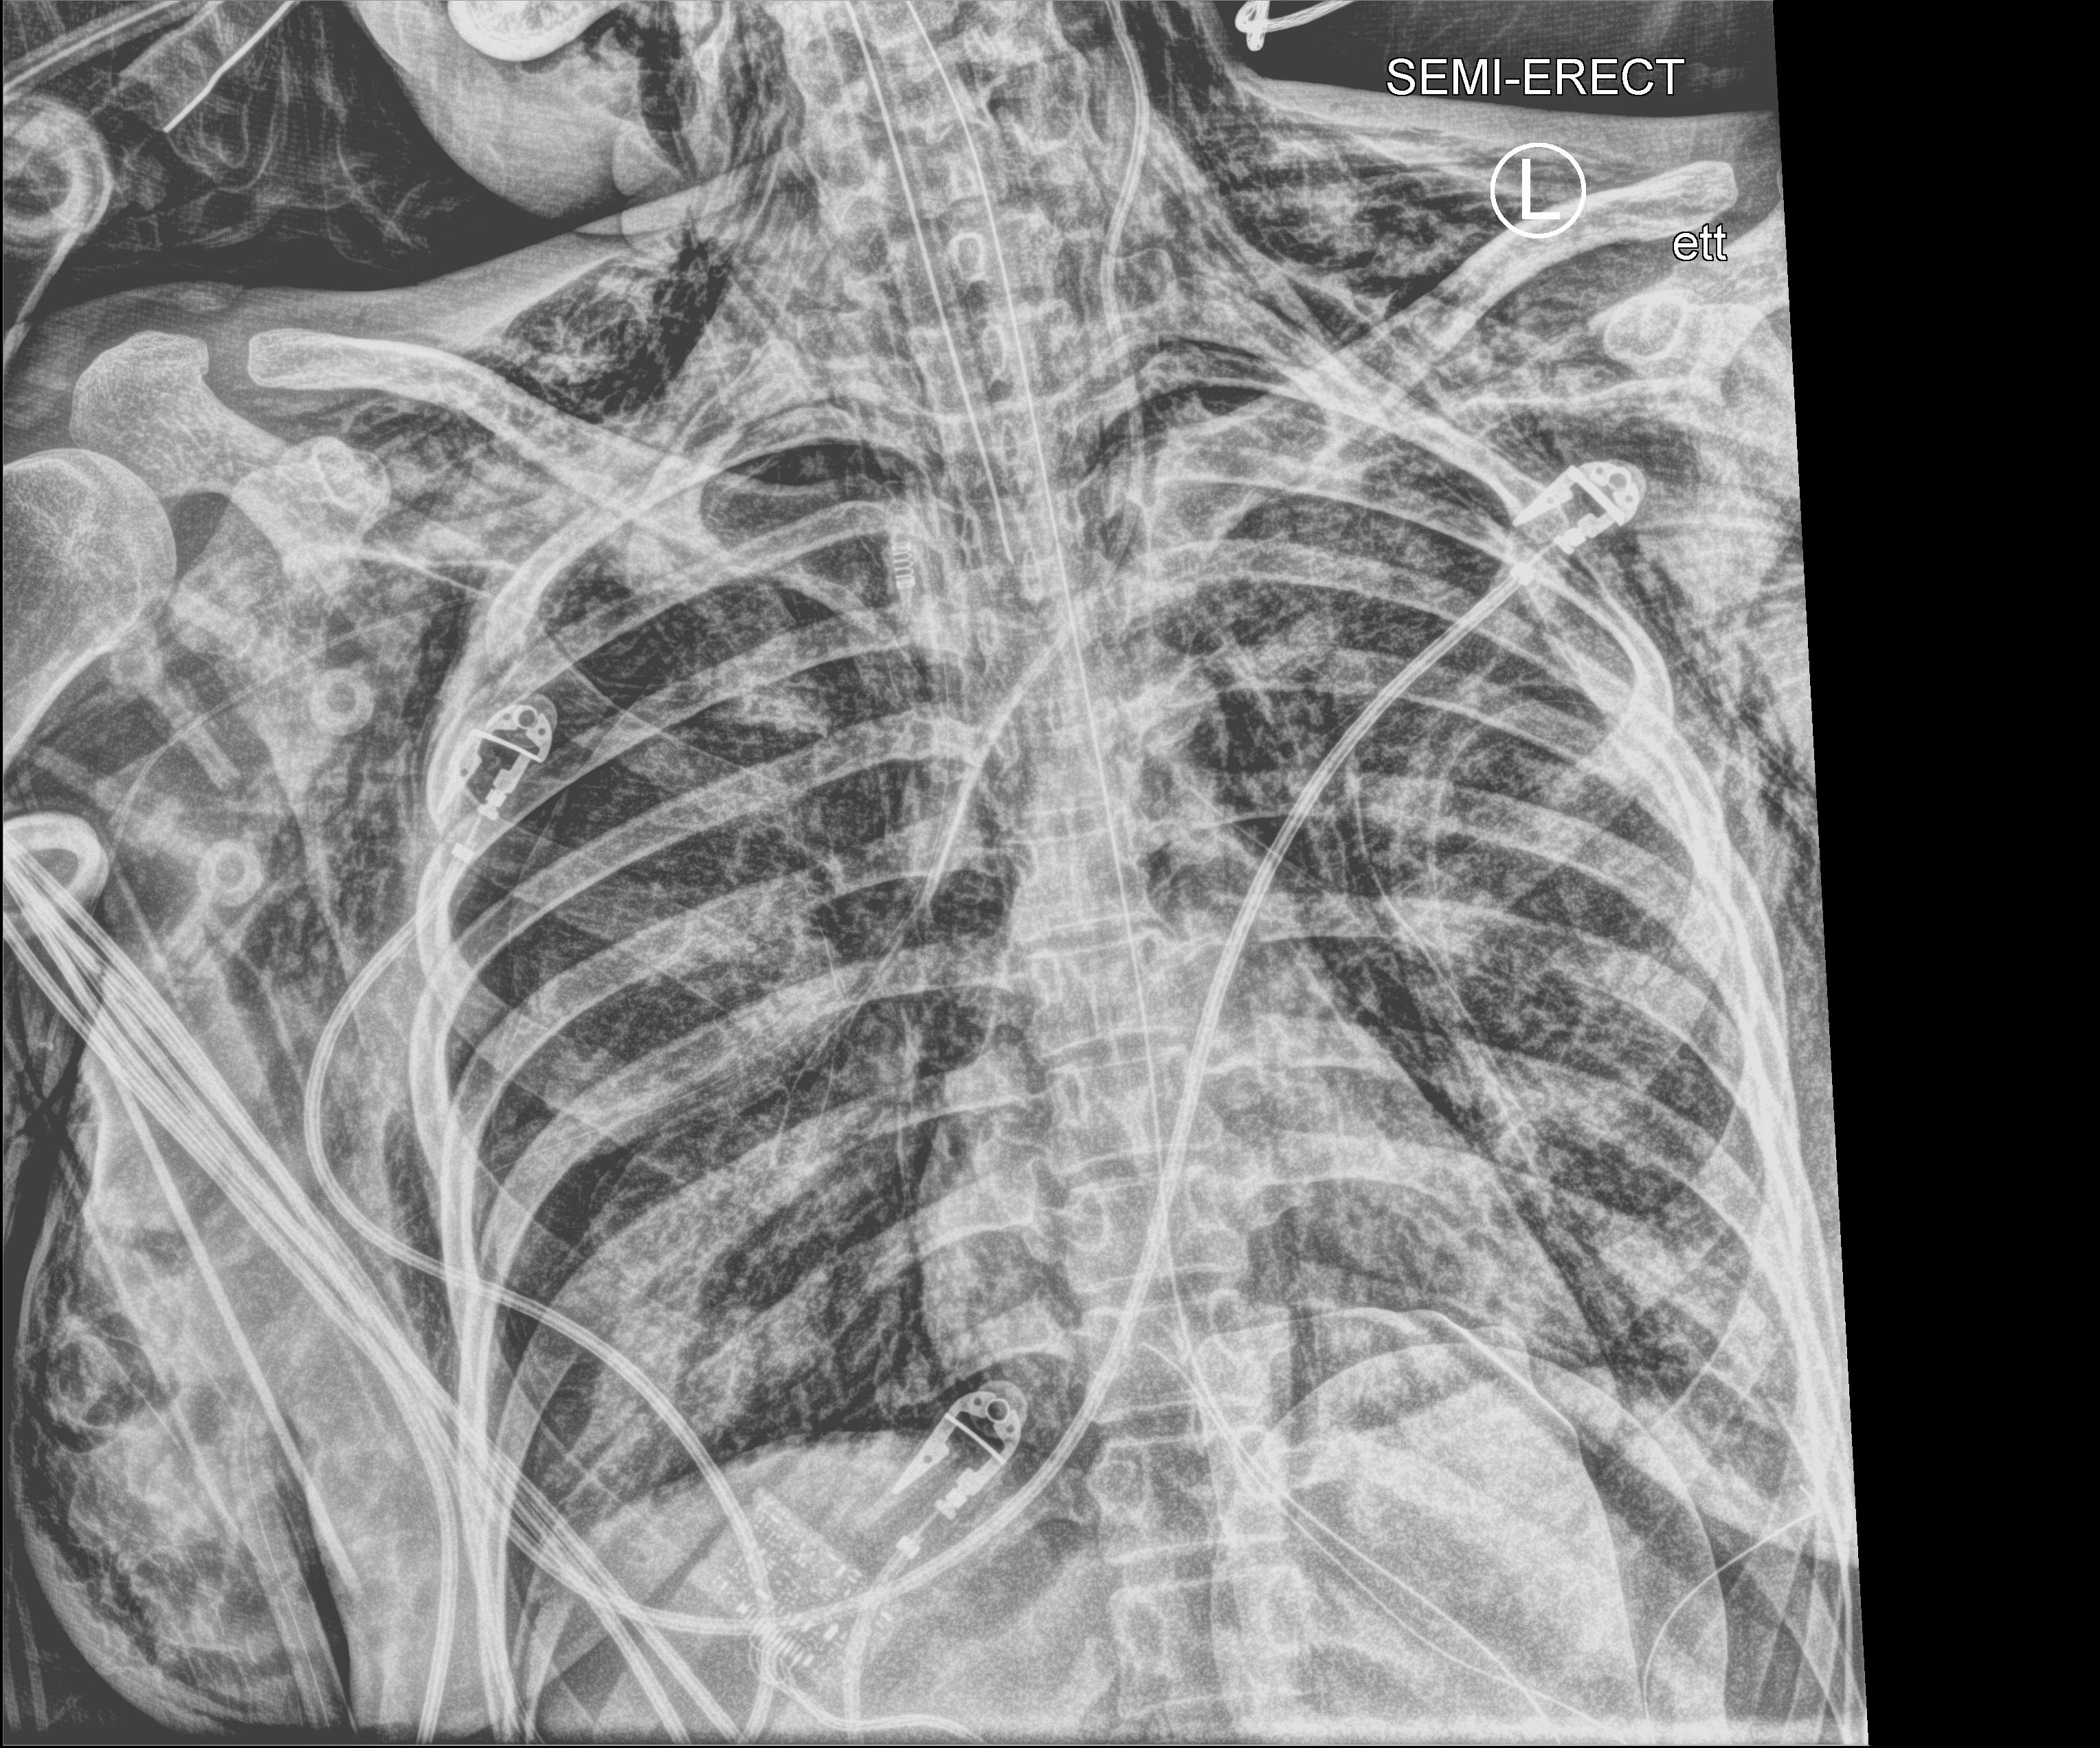
Portable chest radiograph. Patient hospitalised with COVID-19, aged 18–59 years.
From the hospital-stay record, not from the radiograph (when in the stay this image was taken is not recorded): mechanically ventilated during this hospital stay: yes; admitted to intensive care during this hospital stay: yes; chronic kidney disease (admission record): no.